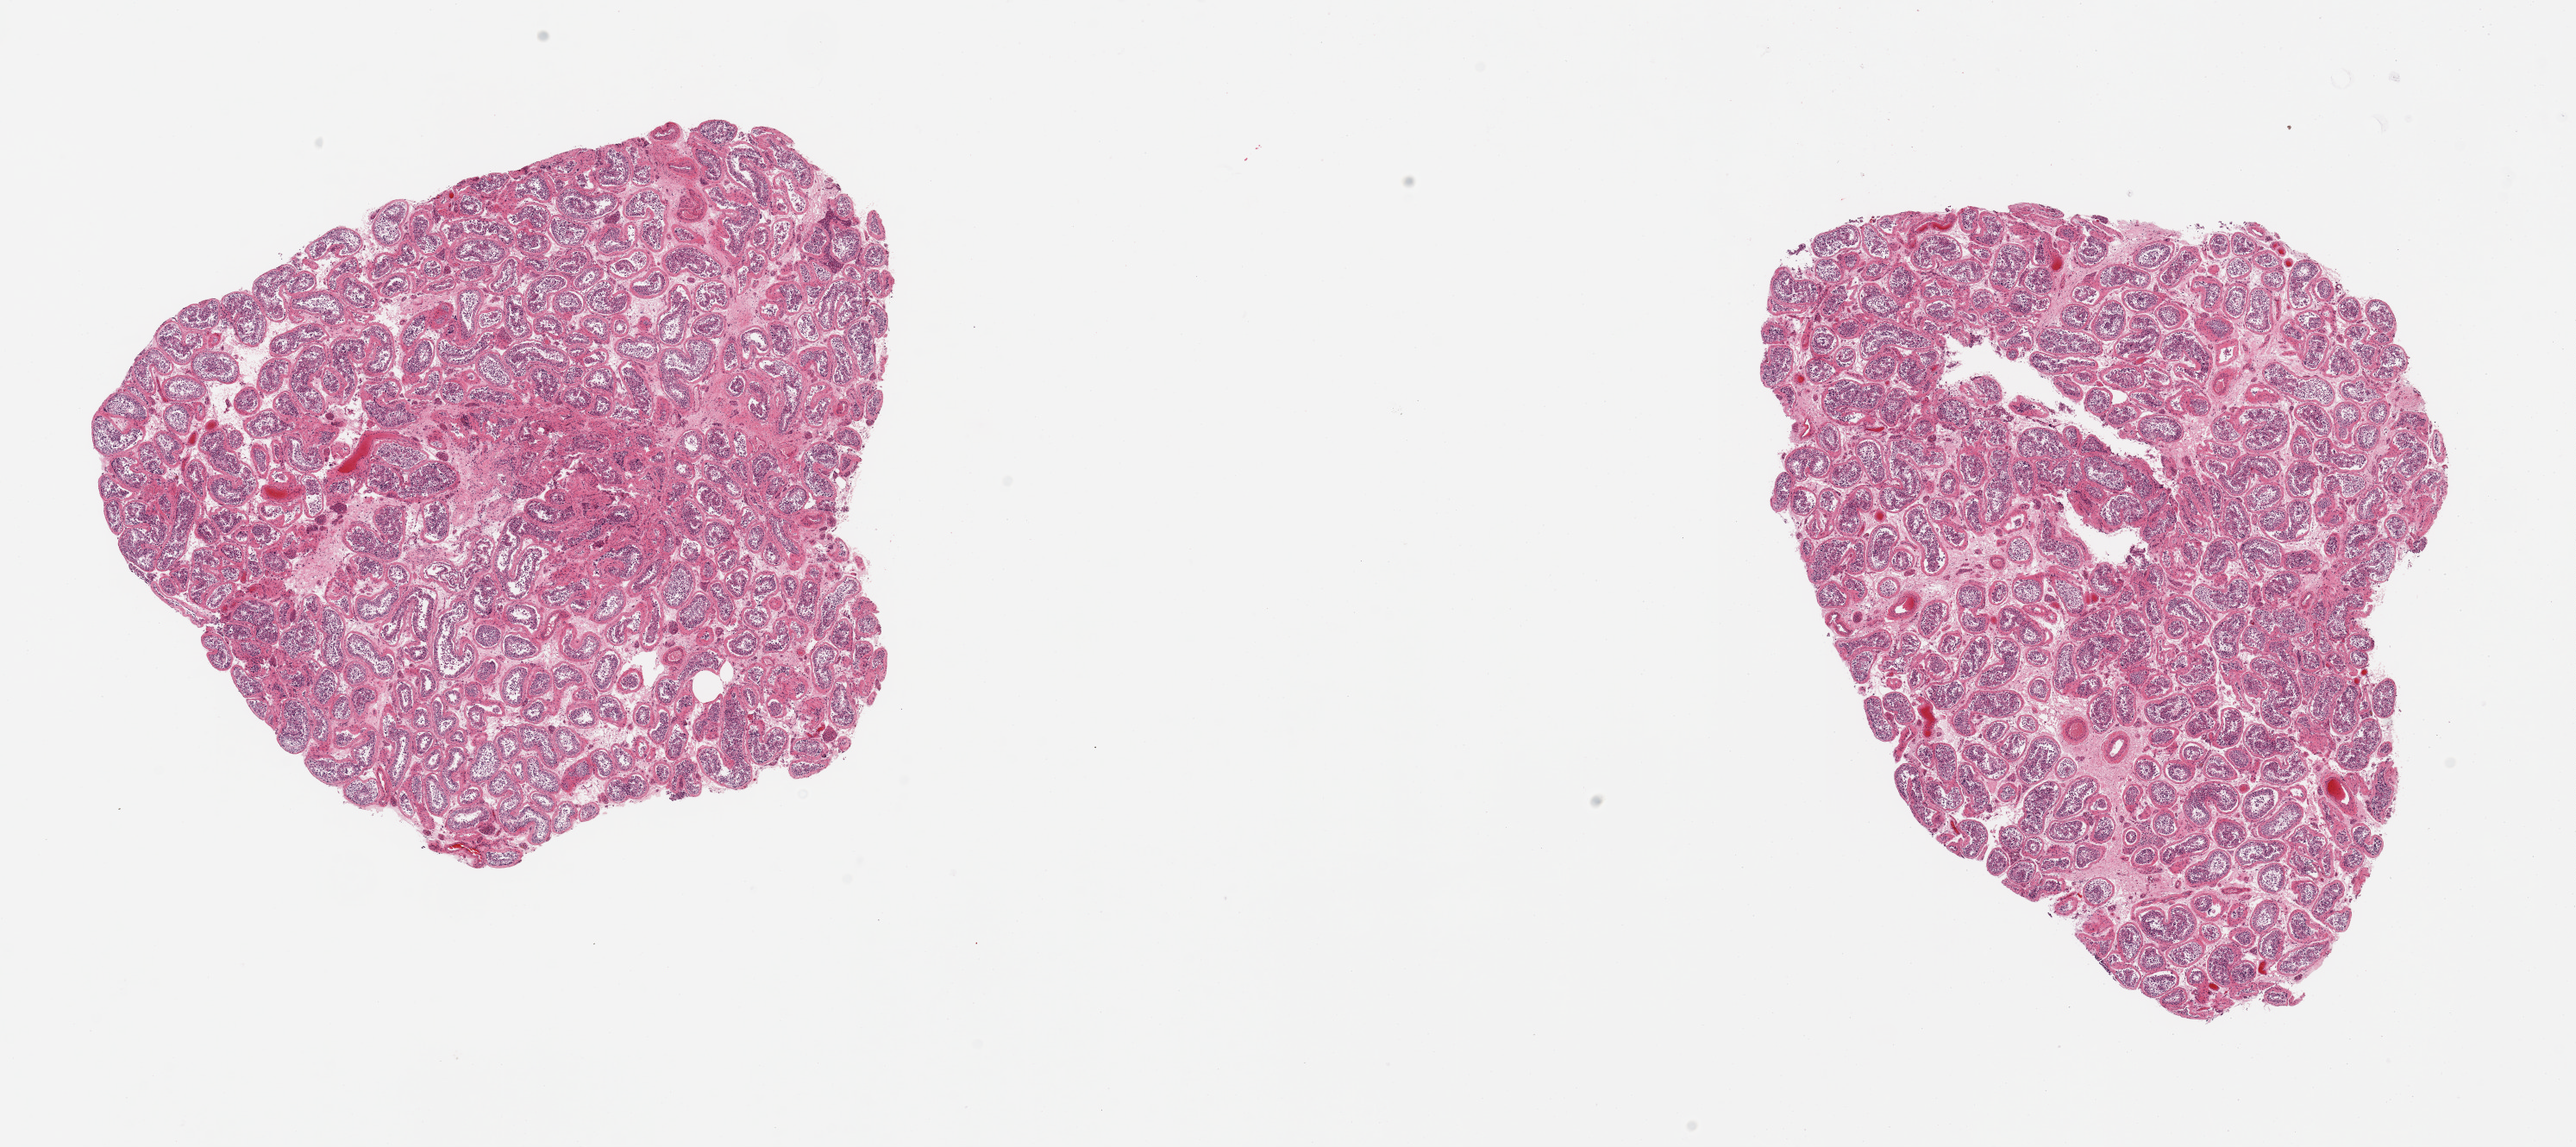
Digitized H&E-stained section, whole scanned area (about 23.6 x 10.5 mm, acquisition: 20x scan) shown as a low-resolution overview, PAXgene-fixed paraffin-embedded (PFPE) section, sampled site (target tissue): testis, donor tissue sample.
Reviewer comment on this tissue sample: 2 pieces; decreased spermatogenesis.